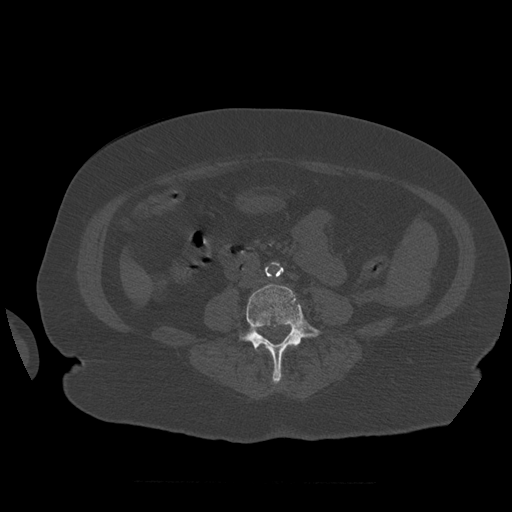
CT including the spine, one axial slice. Position 206 of 399 along the scan axis. Reconstruction kernel STANDARD. Bone window (W 1800 / L 400 HU). 1.25 mm slice thickness. 512 × 512 image matrix. Patient age 81 years. From the clinical record (not read from this slice): primary cancer: renal; vertebrae with lytic lesions (as recorded): L1.
Annotated regions visible in this slice (semi-automatically segmented with operator editing):
- L4 vertebra: bounding box [x1, y1, x2, y2] px = [240, 284, 321, 383]